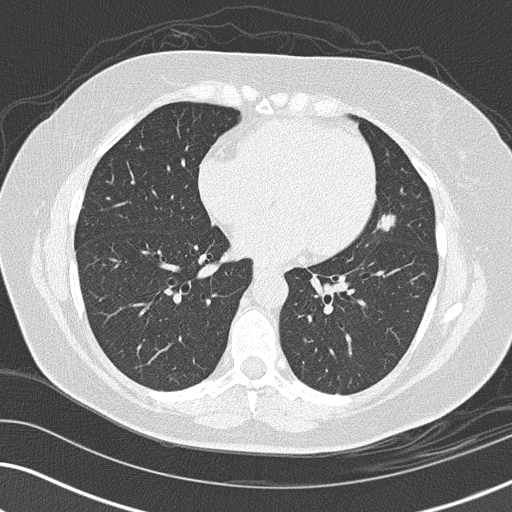
Axial slice from a low-dose chest CT screening exam. Third screening round (two years after baseline). Lung window (W 1500 / L -600 HU). 2 mm slice thickness. Lung (sharp) reconstruction kernel (B50f). Female participant, aged 56 years at enrolment. Former smoker at enrolment.
Lesion marked by an expert reader, box from (x=355, y=200) to (x=411, y=250) px. Screening reader's record for this exam (one nodule recorded; not confirmed to be the boxed lesion): non-calcified nodule or mass ≥4 mm, lingula, 14 × 14 mm, spiculated (stellate) margins, soft tissue attenuation, pre-existing on the prior screen: yes; interval growth: yes.